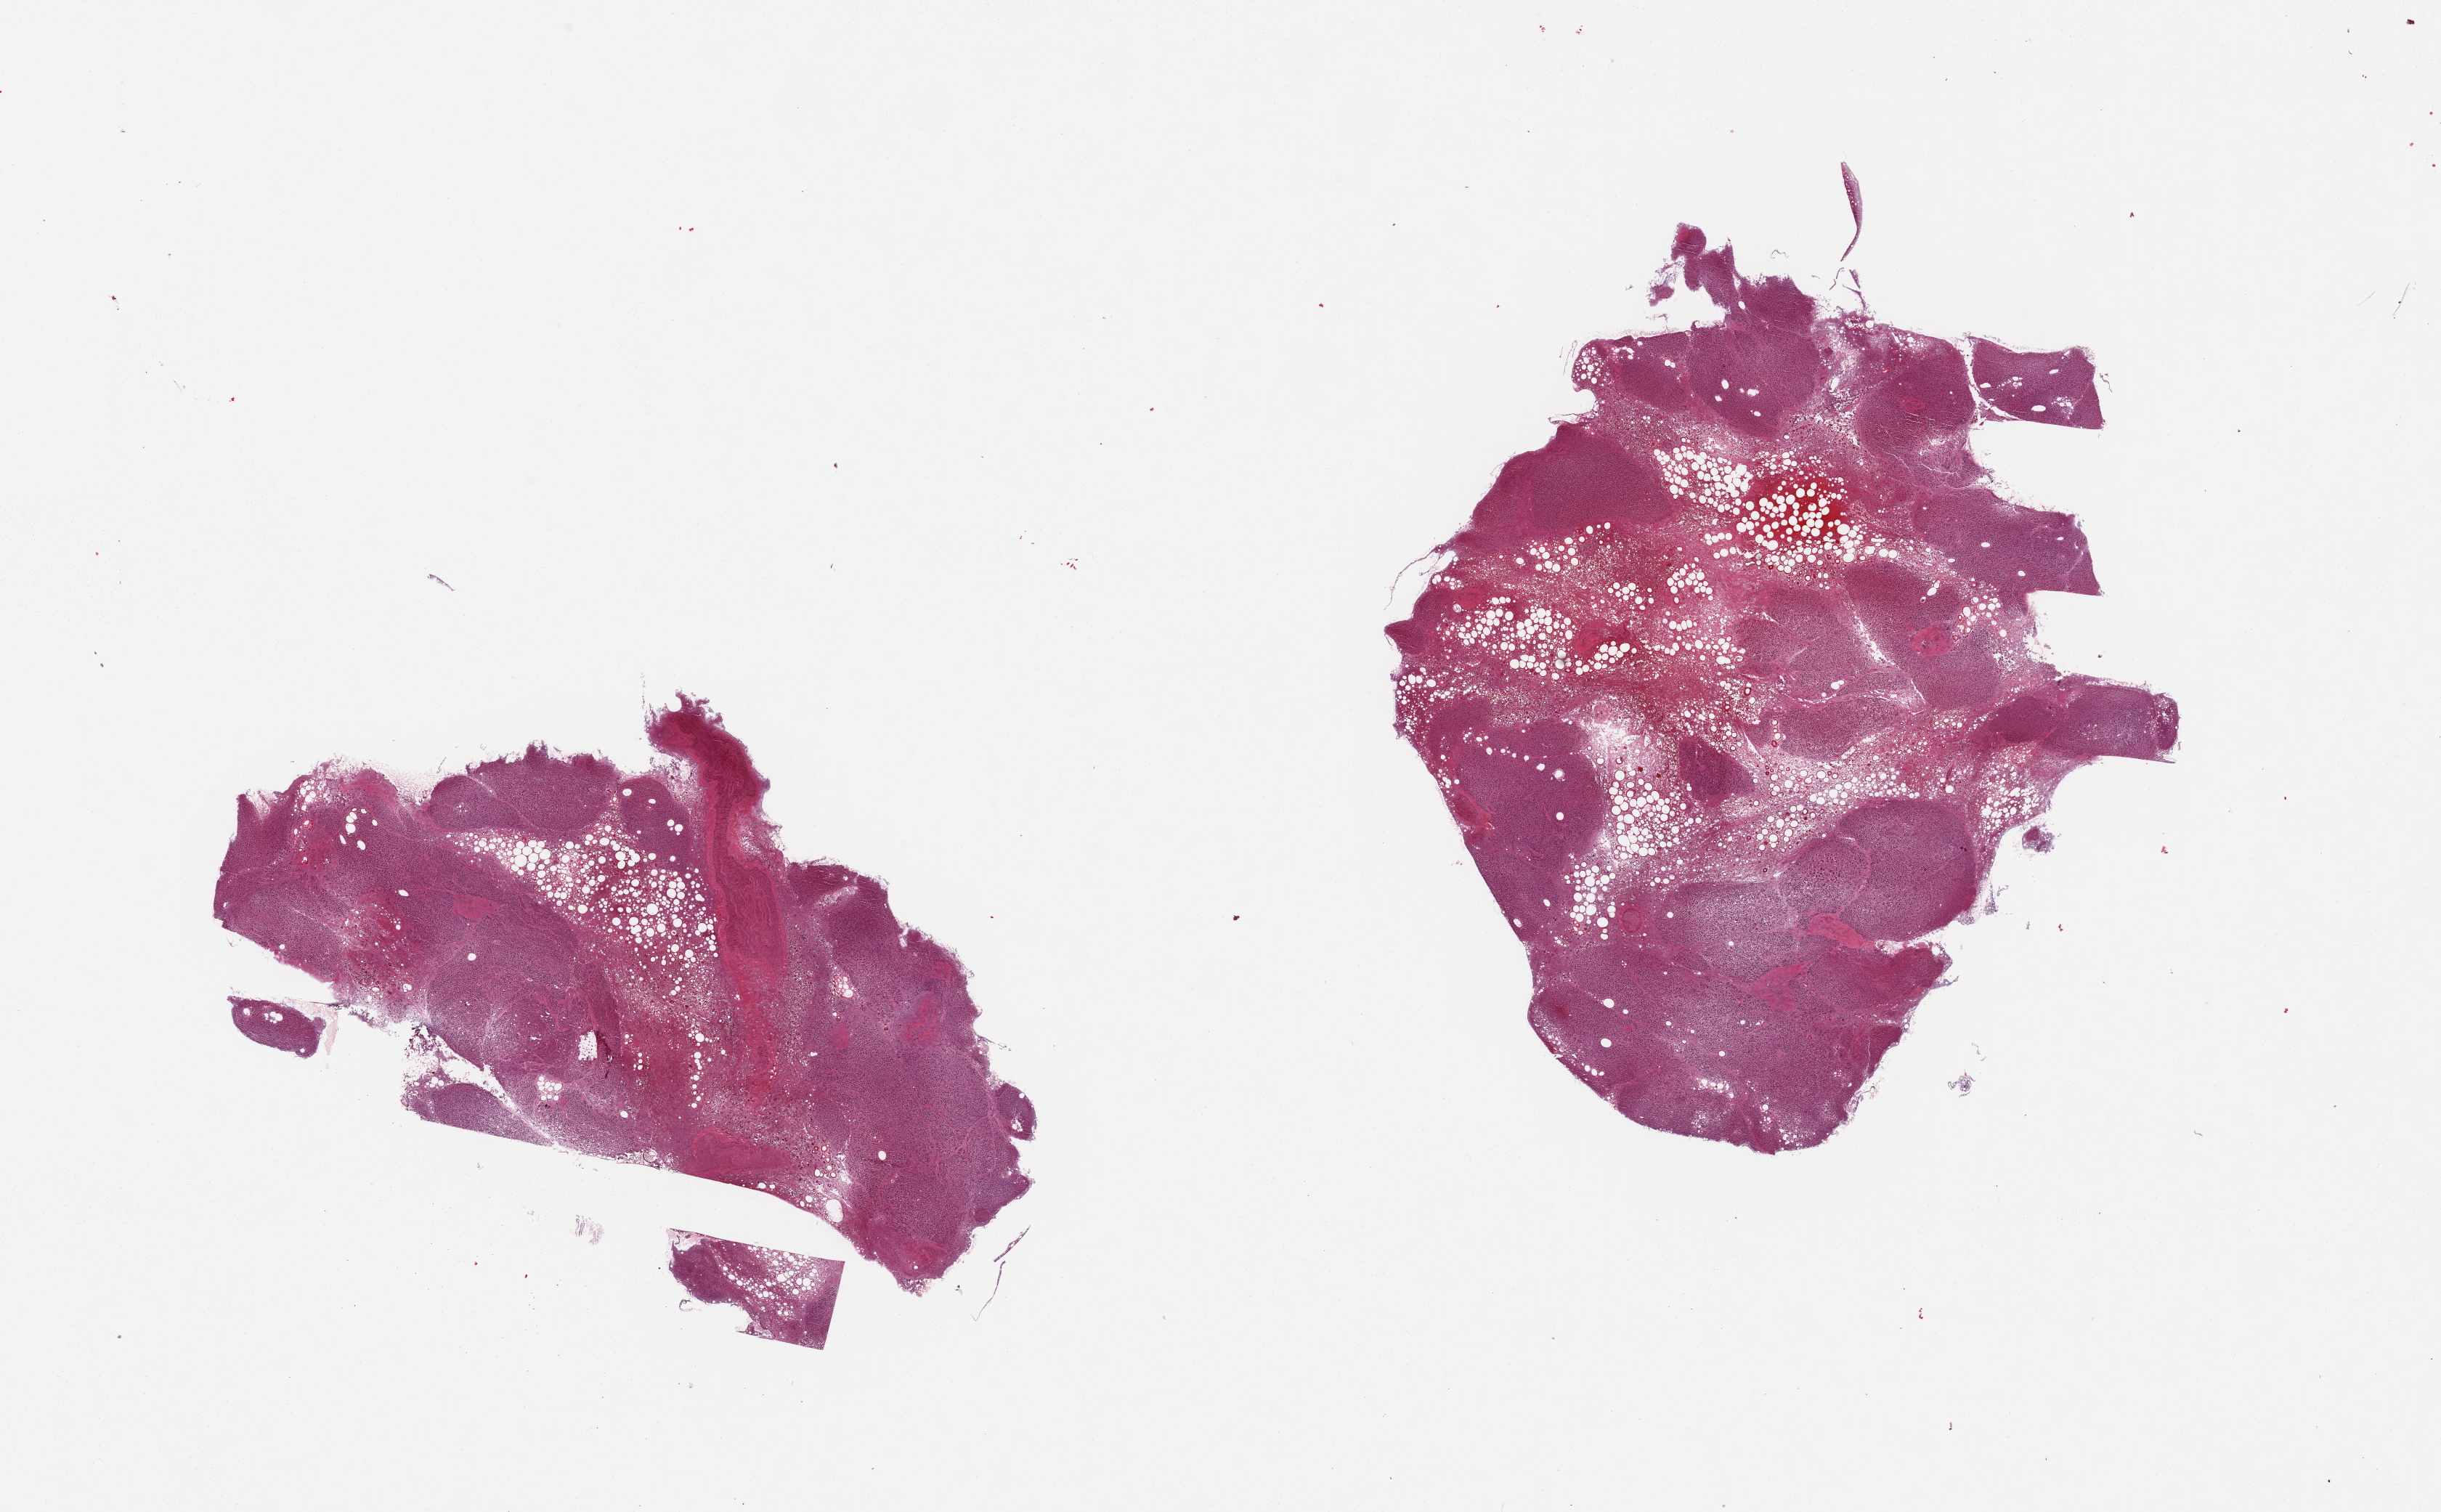
Digitized hematoxylin and eosin (H&E)-stained section, shown as a low-resolution overview of the whole scanned area (about 26.6 x 16.5 mm). PAXgene-fixed, paraffin-embedded tissue. Sampled site (target tissue): pancreas. Tissue donor sample.
• reviewer comment on this tissue sample: 2 pieces; 50% internal fat